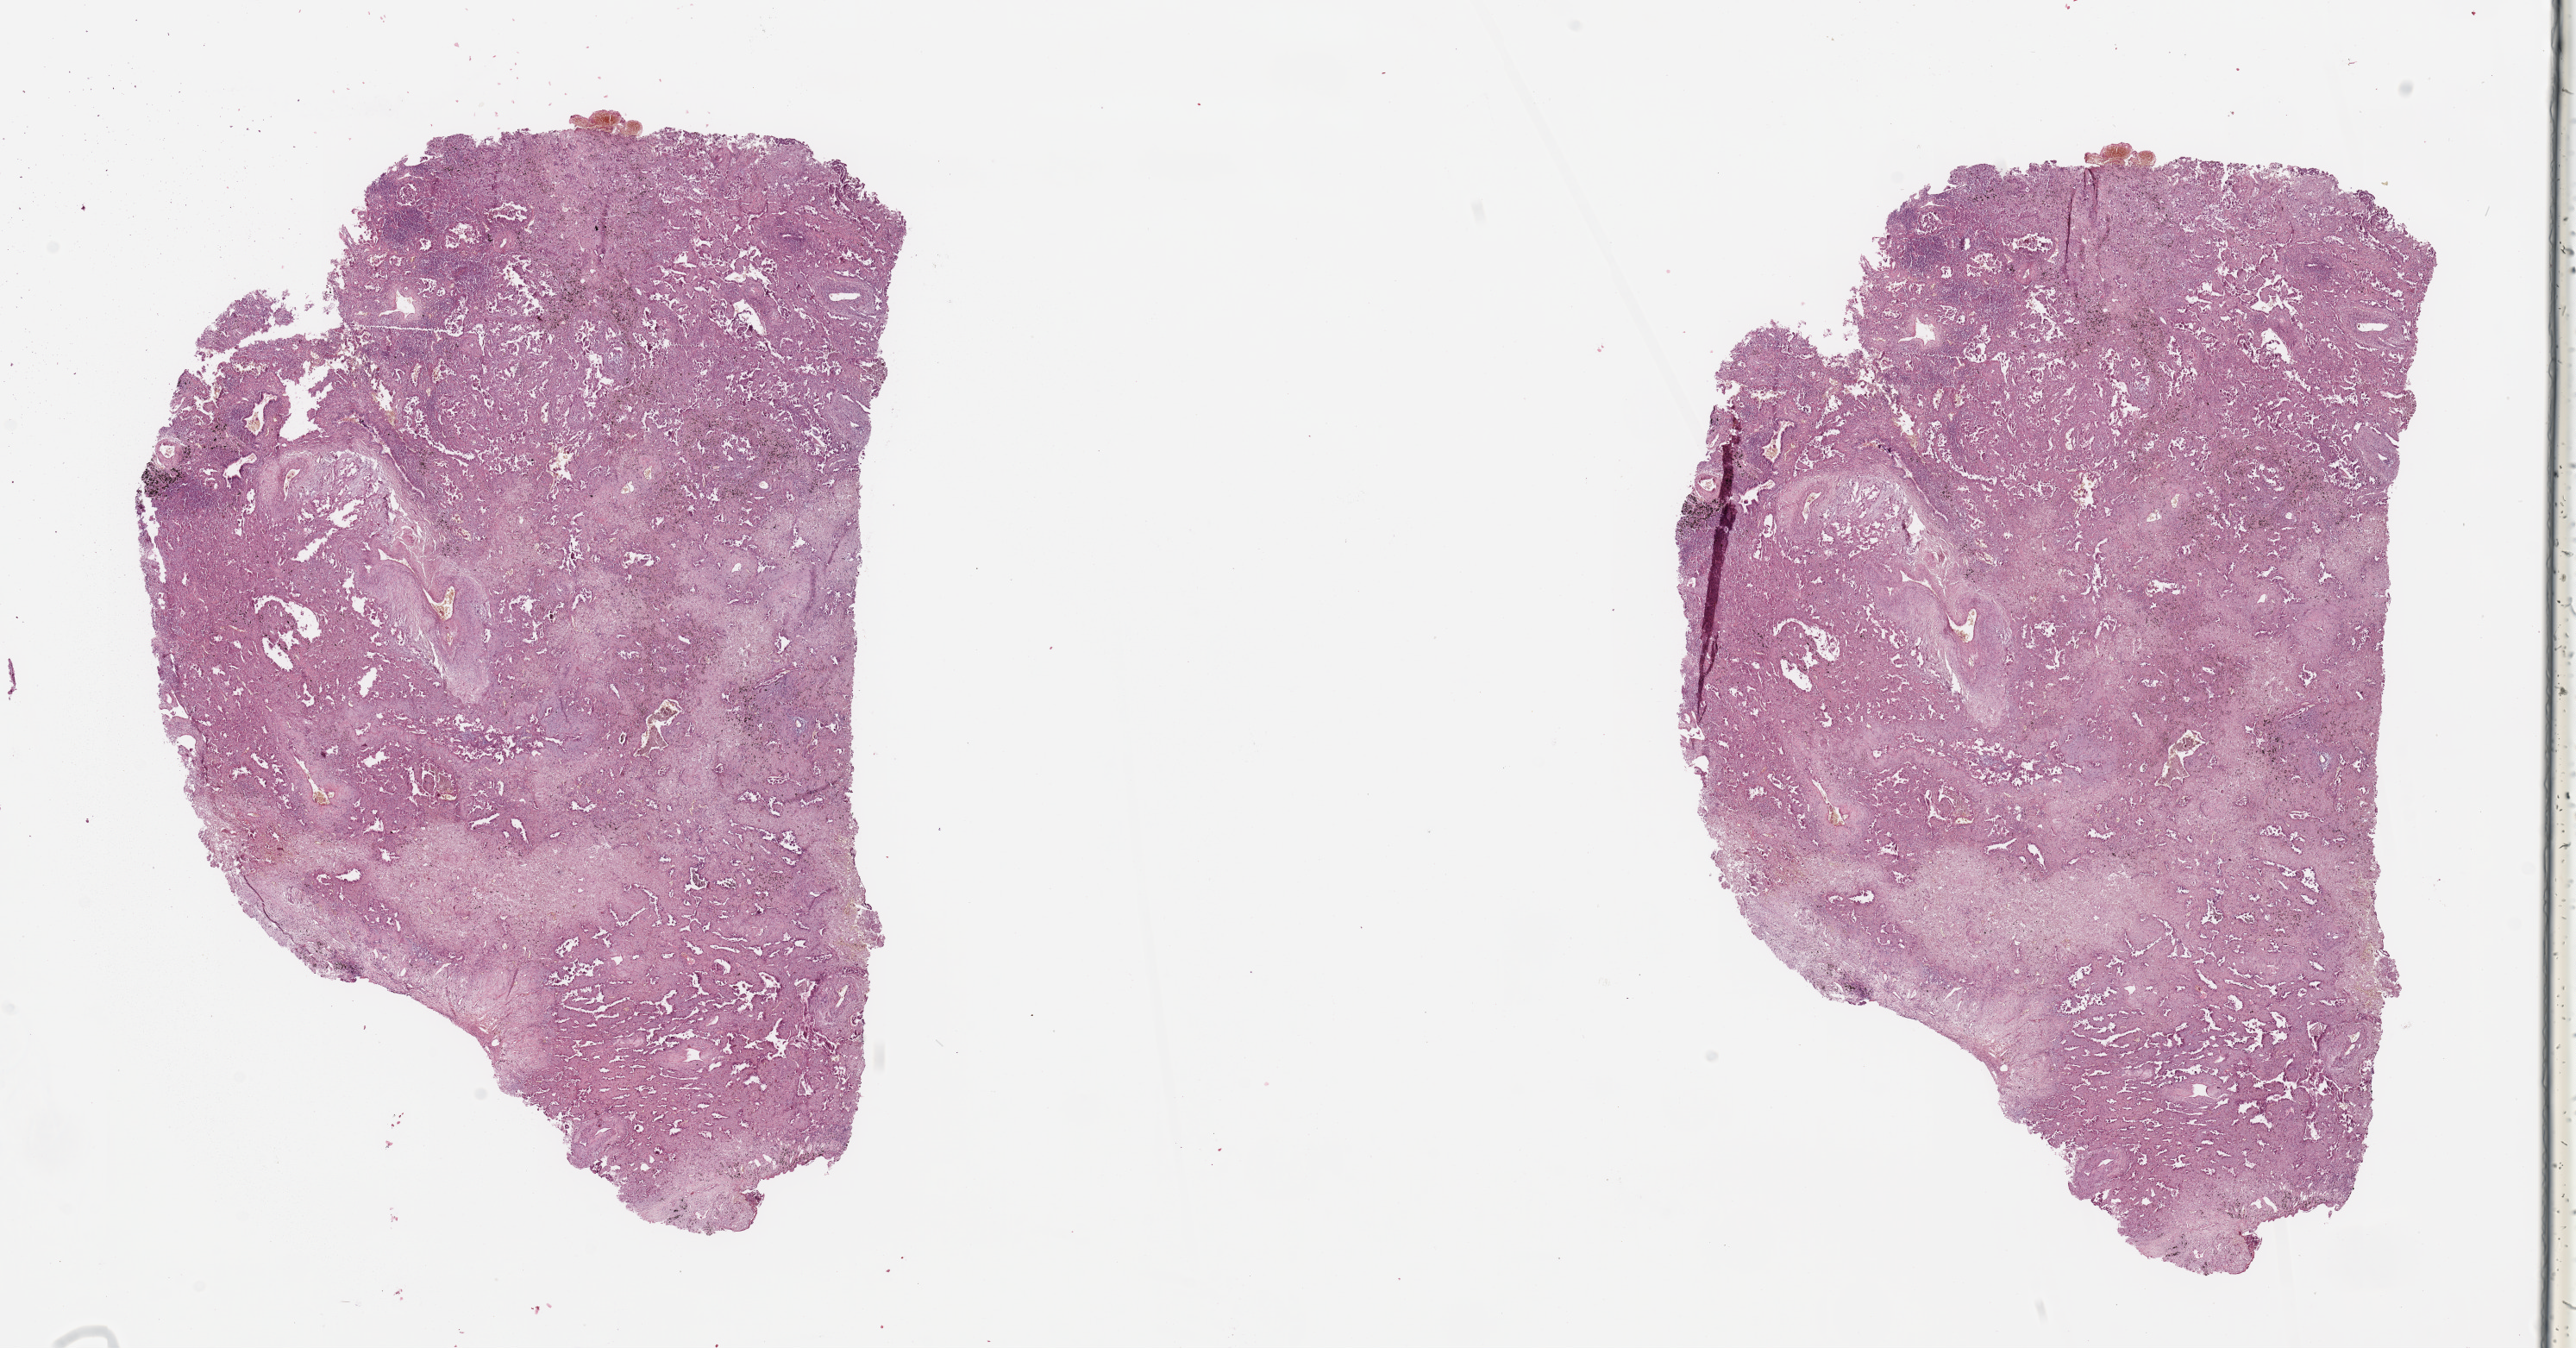
Digitized H&E-stained tissue section (whole slide), a low-resolution overview of the entire scanned area, about 23.6 x 12.4 mm (acquisition: 20x scan), tumour tissue sample, lung. 56-year-old male patient. Histologic grade: G2 (moderately differentiated).
Primary tumour site (as recorded): left upper lobe. Diagnosis: Adenocarcinoma, NOS. AJCC pathologic stage: IIIA.